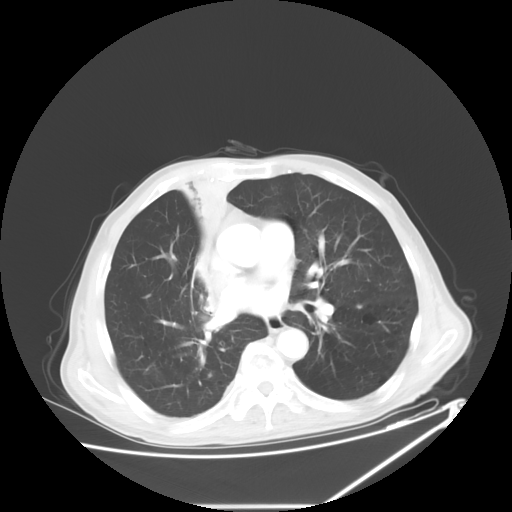
Chest CT, one axial slice. Position 33 of 60 along the scan axis. 120 kVp. Lung window (W 1500 / L -600 HU). 5 mm slice thickness. 512 × 512 image matrix. Patient: male, 73 years. Case-level facts recorded for this patient, not image findings: clinical TNM (as recorded): T2a N1 M0.
Outlined on this slice (rectangle marked by the reading radiologist):
- lung tumour (recorded histology: squamous cell carcinoma): bounding box <178,160,226,276> (left, top, right, bottom; pixels)